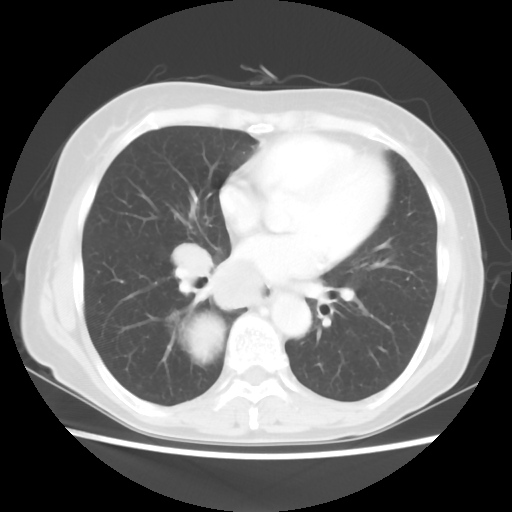
Chest CT, one axial slice. Position 24 of 56 along the scan axis. Lung window (W 1500 / L -600 HU). 512 × 512 image matrix, field of view 332 × 332 mm. Female patient, age 66 years. From the clinical record (not read from this slice): clinical TNM (as recorded): T2 N3 M0; histopathological grade: G3.
Structures marked on this image (rectangle marked by the reading radiologist):
- lung tumour (recorded histology: small cell carcinoma): box from (x=187, y=312) to (x=224, y=369) px